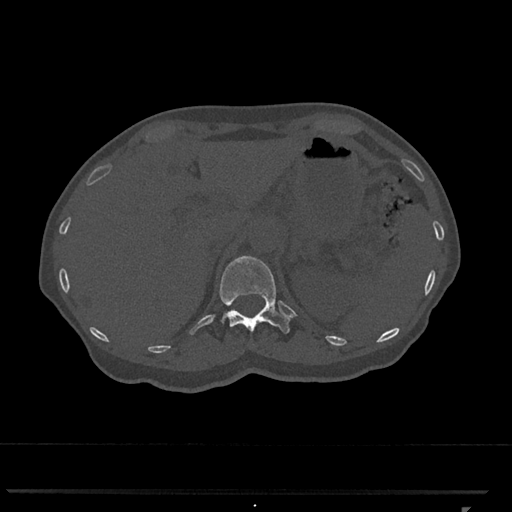
CT including the spine, one axial slice. Slice 461 of 793 in the series (ordered by position). 120 kVp. Bone window (W 1800 / L 400 HU). 512 × 512 image matrix. Female patient, age 62 years. From the clinical record (not read from this slice): primary cancer: renal.
Structures marked on this image (semi-automatic segmentation, software-assisted and operator-edited):
- T12 vertebra: box from (x=219, y=256) to (x=290, y=334) px